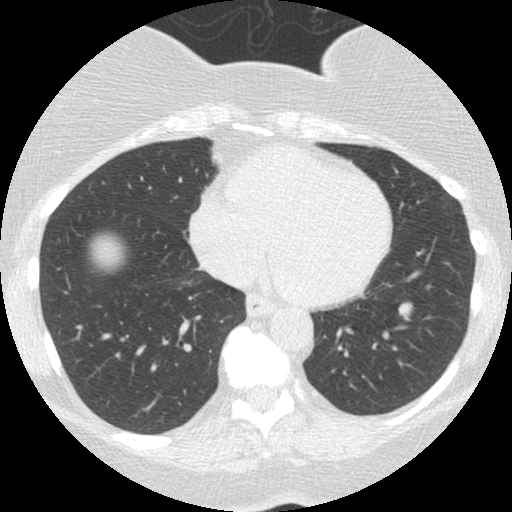
Low-dose screening chest CT, one axial slice; position 59 of 167 along the scan axis; reconstruction kernel STANDARD; lung window (W 1500 / L -600 HU); 512 × 512 image matrix, field of view 300 × 300 mm.
Annotated regions visible in this slice (outlined manually by an expert reader):
- lesion 1 (tumor, lower lobe of left lung): bounding box [x1, y1, x2, y2] px = [399, 303, 412, 320]